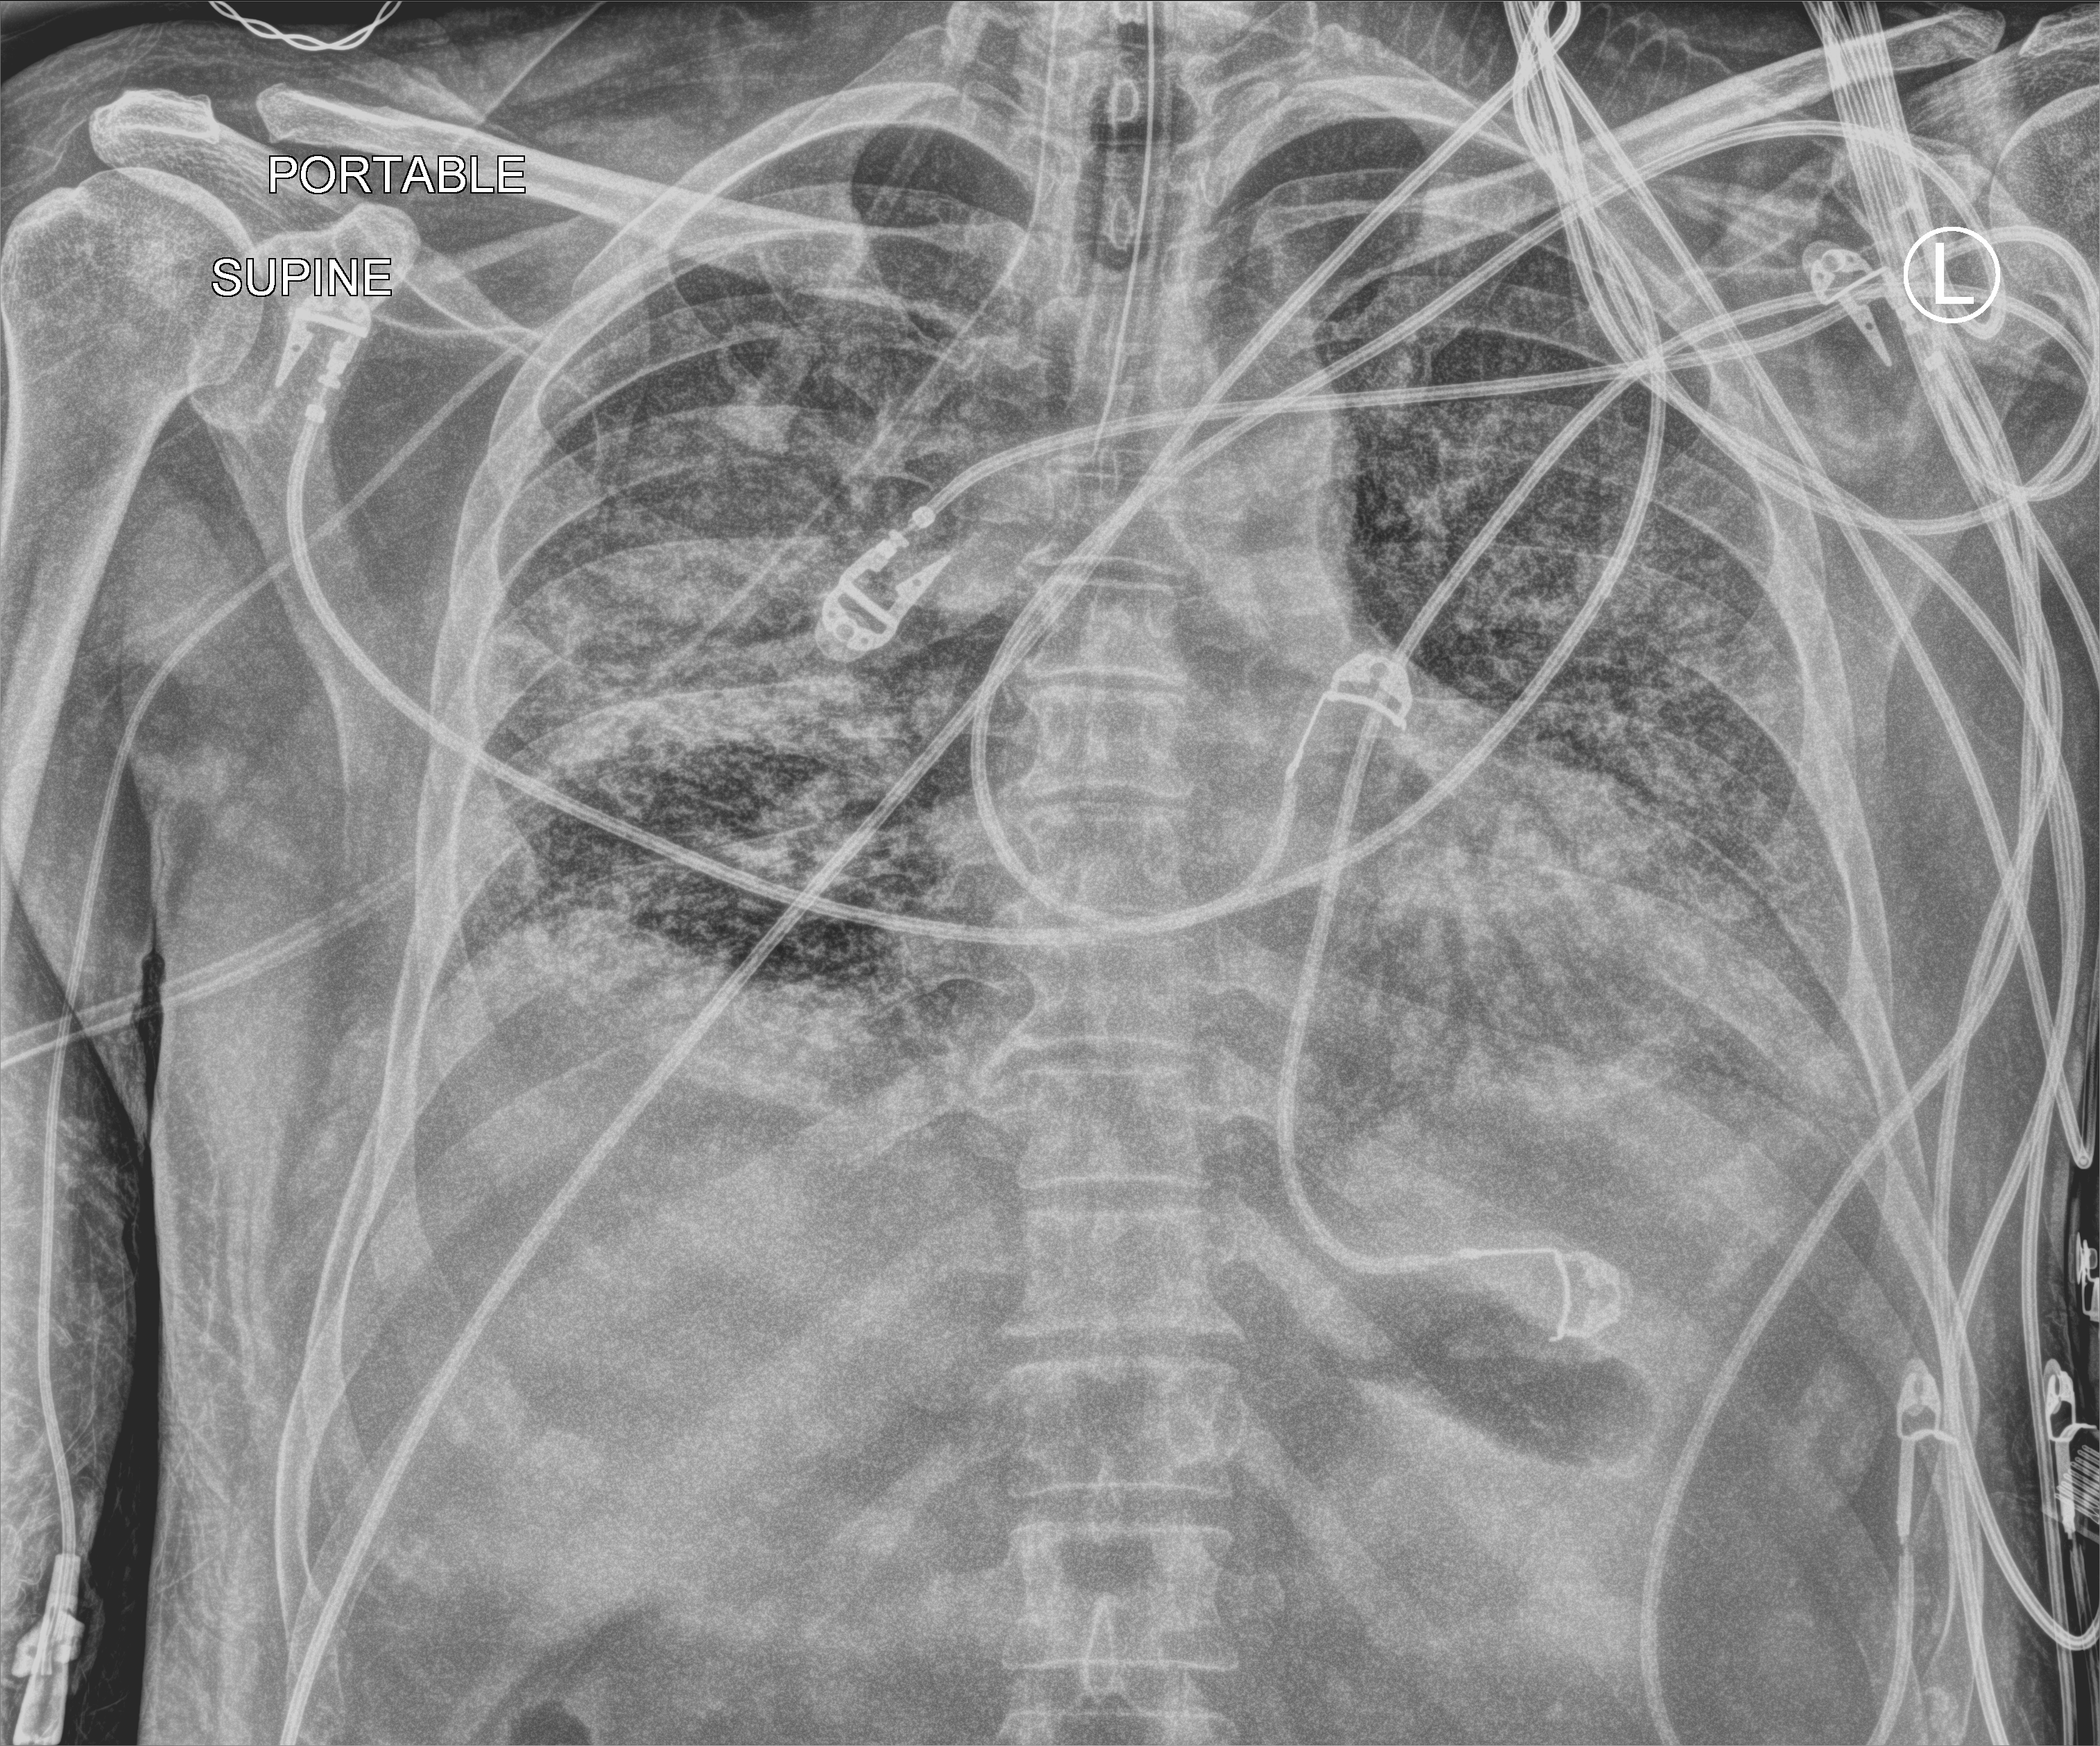
Chest X-ray (portable); anteroposterior (AP) projection. Patient hospitalised with COVID-19; male, aged 18–59 years.
Admission-level facts for this patient (not findings on this image; timing relative to this image not recorded): mechanically ventilated during this hospital stay: yes.